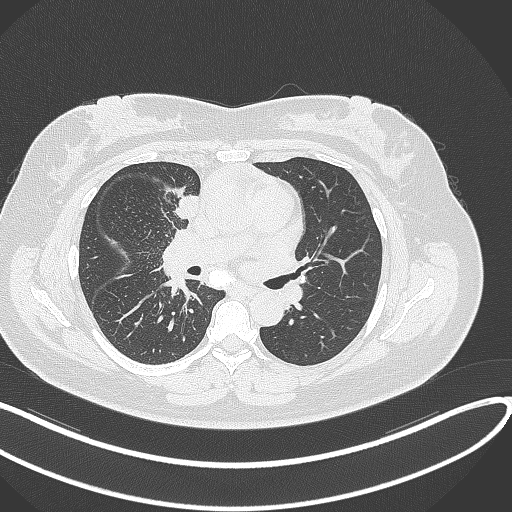
Chest CT, one axial slice. Position 148 of 303 along the scan axis. Reconstruction kernel B70f. Lung window (W 1500 / L -600 HU). 1 mm slice thickness. 512 × 512 image matrix, field of view 400 × 400 mm. Patient: female, 46 years. Case-level facts recorded for this patient, not image findings: clinical TNM (as recorded): T2a N1 M0.
Outlined on this slice (rectangle marked by the reading radiologist):
- lung tumour (recorded histology: adenocarcinoma): bounding box <172,193,205,223> (left, top, right, bottom; pixels)